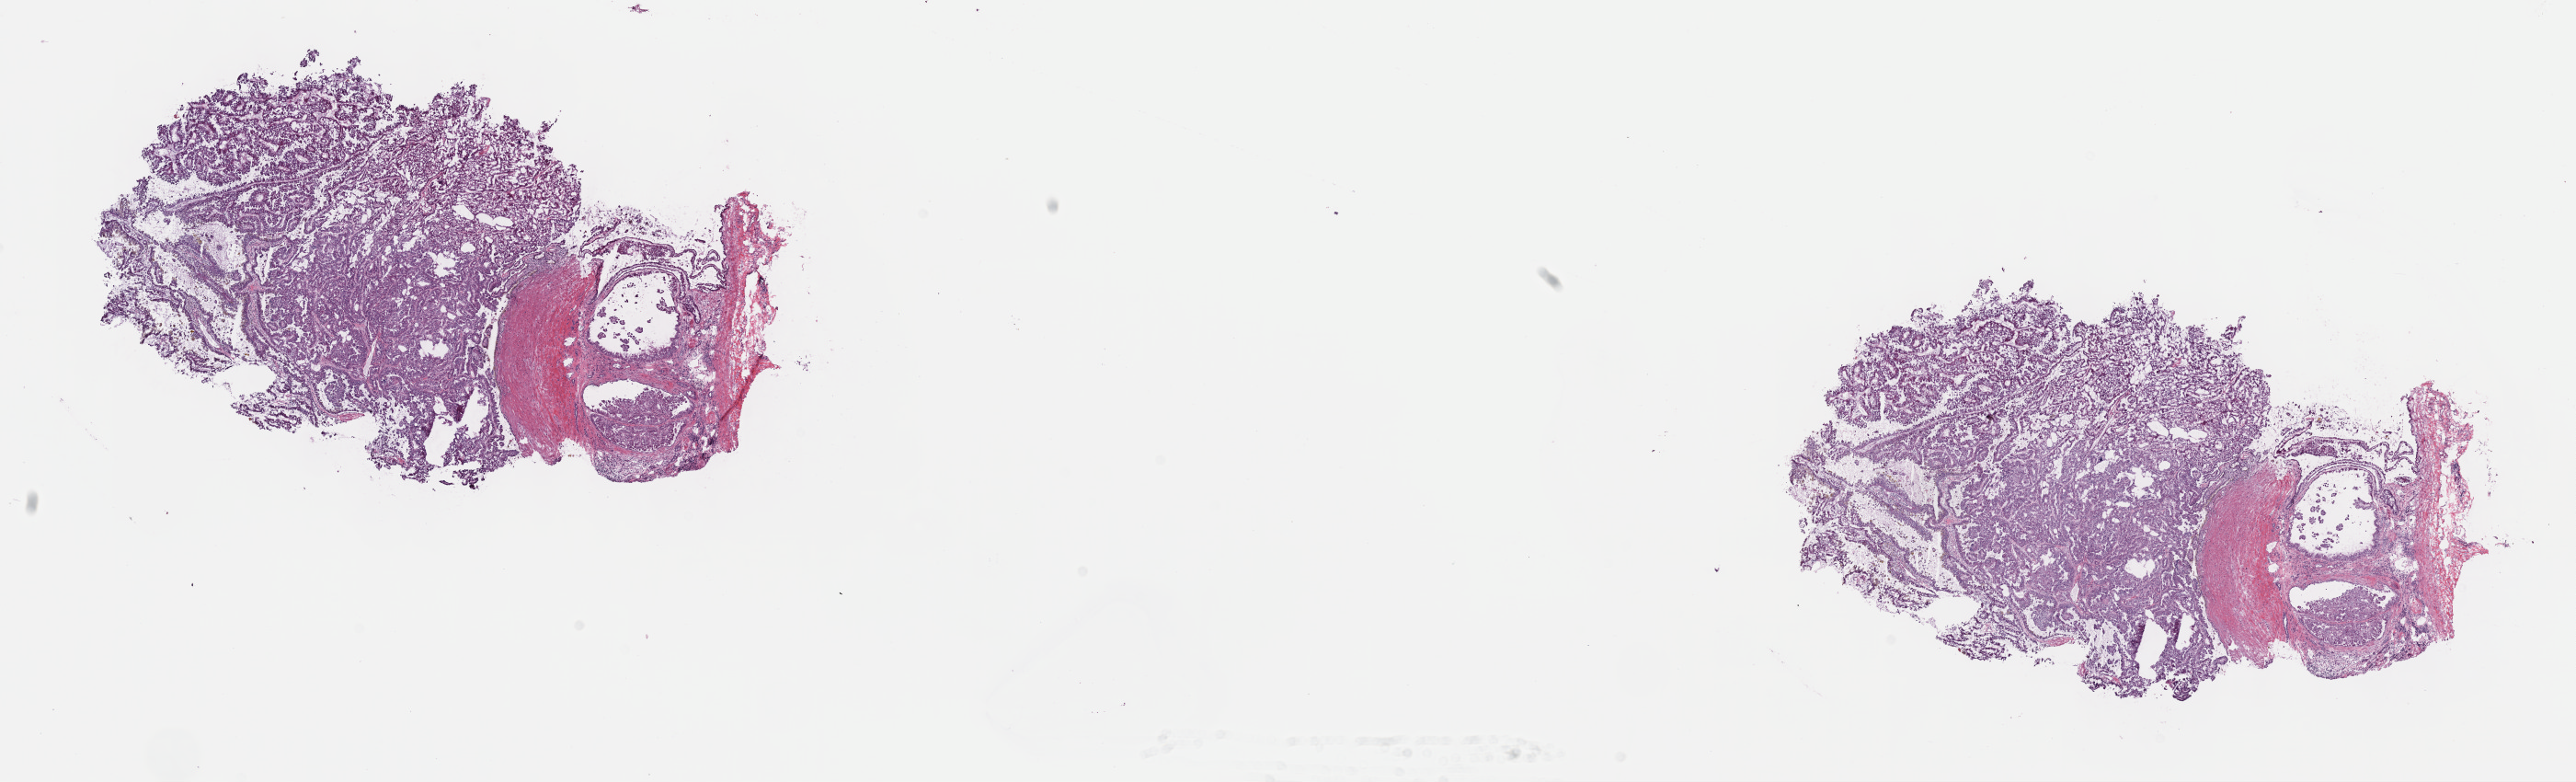
Digitized H&E-stained tissue section (whole slide), low-resolution overview of the scanned area, about 22.7 x 6.9 mm (slide scanned at 40x), frozen section from the top of the tissue portion, kidney, primary tumour sample. Male patient; age at initial diagnosis 74 years. Slide review estimates, as recorded: tumour cells 70%, tumour nuclei 70%, normal cells 0%, stromal cells 30%, necrosis 0%. Infiltration values recorded for this section: lymphocyte infiltration 2%, monocyte infiltration 5%, neutrophil infiltration 0%.
• TNM: T1b NX MX
• histologic diagnosis: Papillary adenocarcinoma, NOS
• AJCC pathologic stage: I (7th edition)